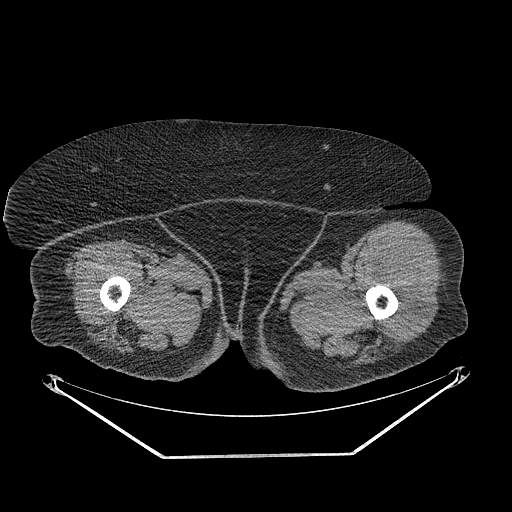
CT of an extremity soft-tissue mass (from a PET/CT study), one axial slice; position 253 of 267 along the scan axis; soft-tissue window (W 400 / L 40 HU); 512 × 512 image matrix, field of view 500 × 500 mm. Female patient. Case-level facts recorded for this patient, not image findings: histological type: undifferentiated – high grade; grade: high; site of the primary tumour: left thigh.
Annotated regions visible in this slice (expert contour drawn on MRI and transferred to this co-registered scan by the dataset authors):
- gross tumour volume including surrounding oedema: bounding box (x1, y1, x2, y2) in pixels: (377, 253, 426, 336)
- gross tumour volume (mass): (379, 253, 423, 336)